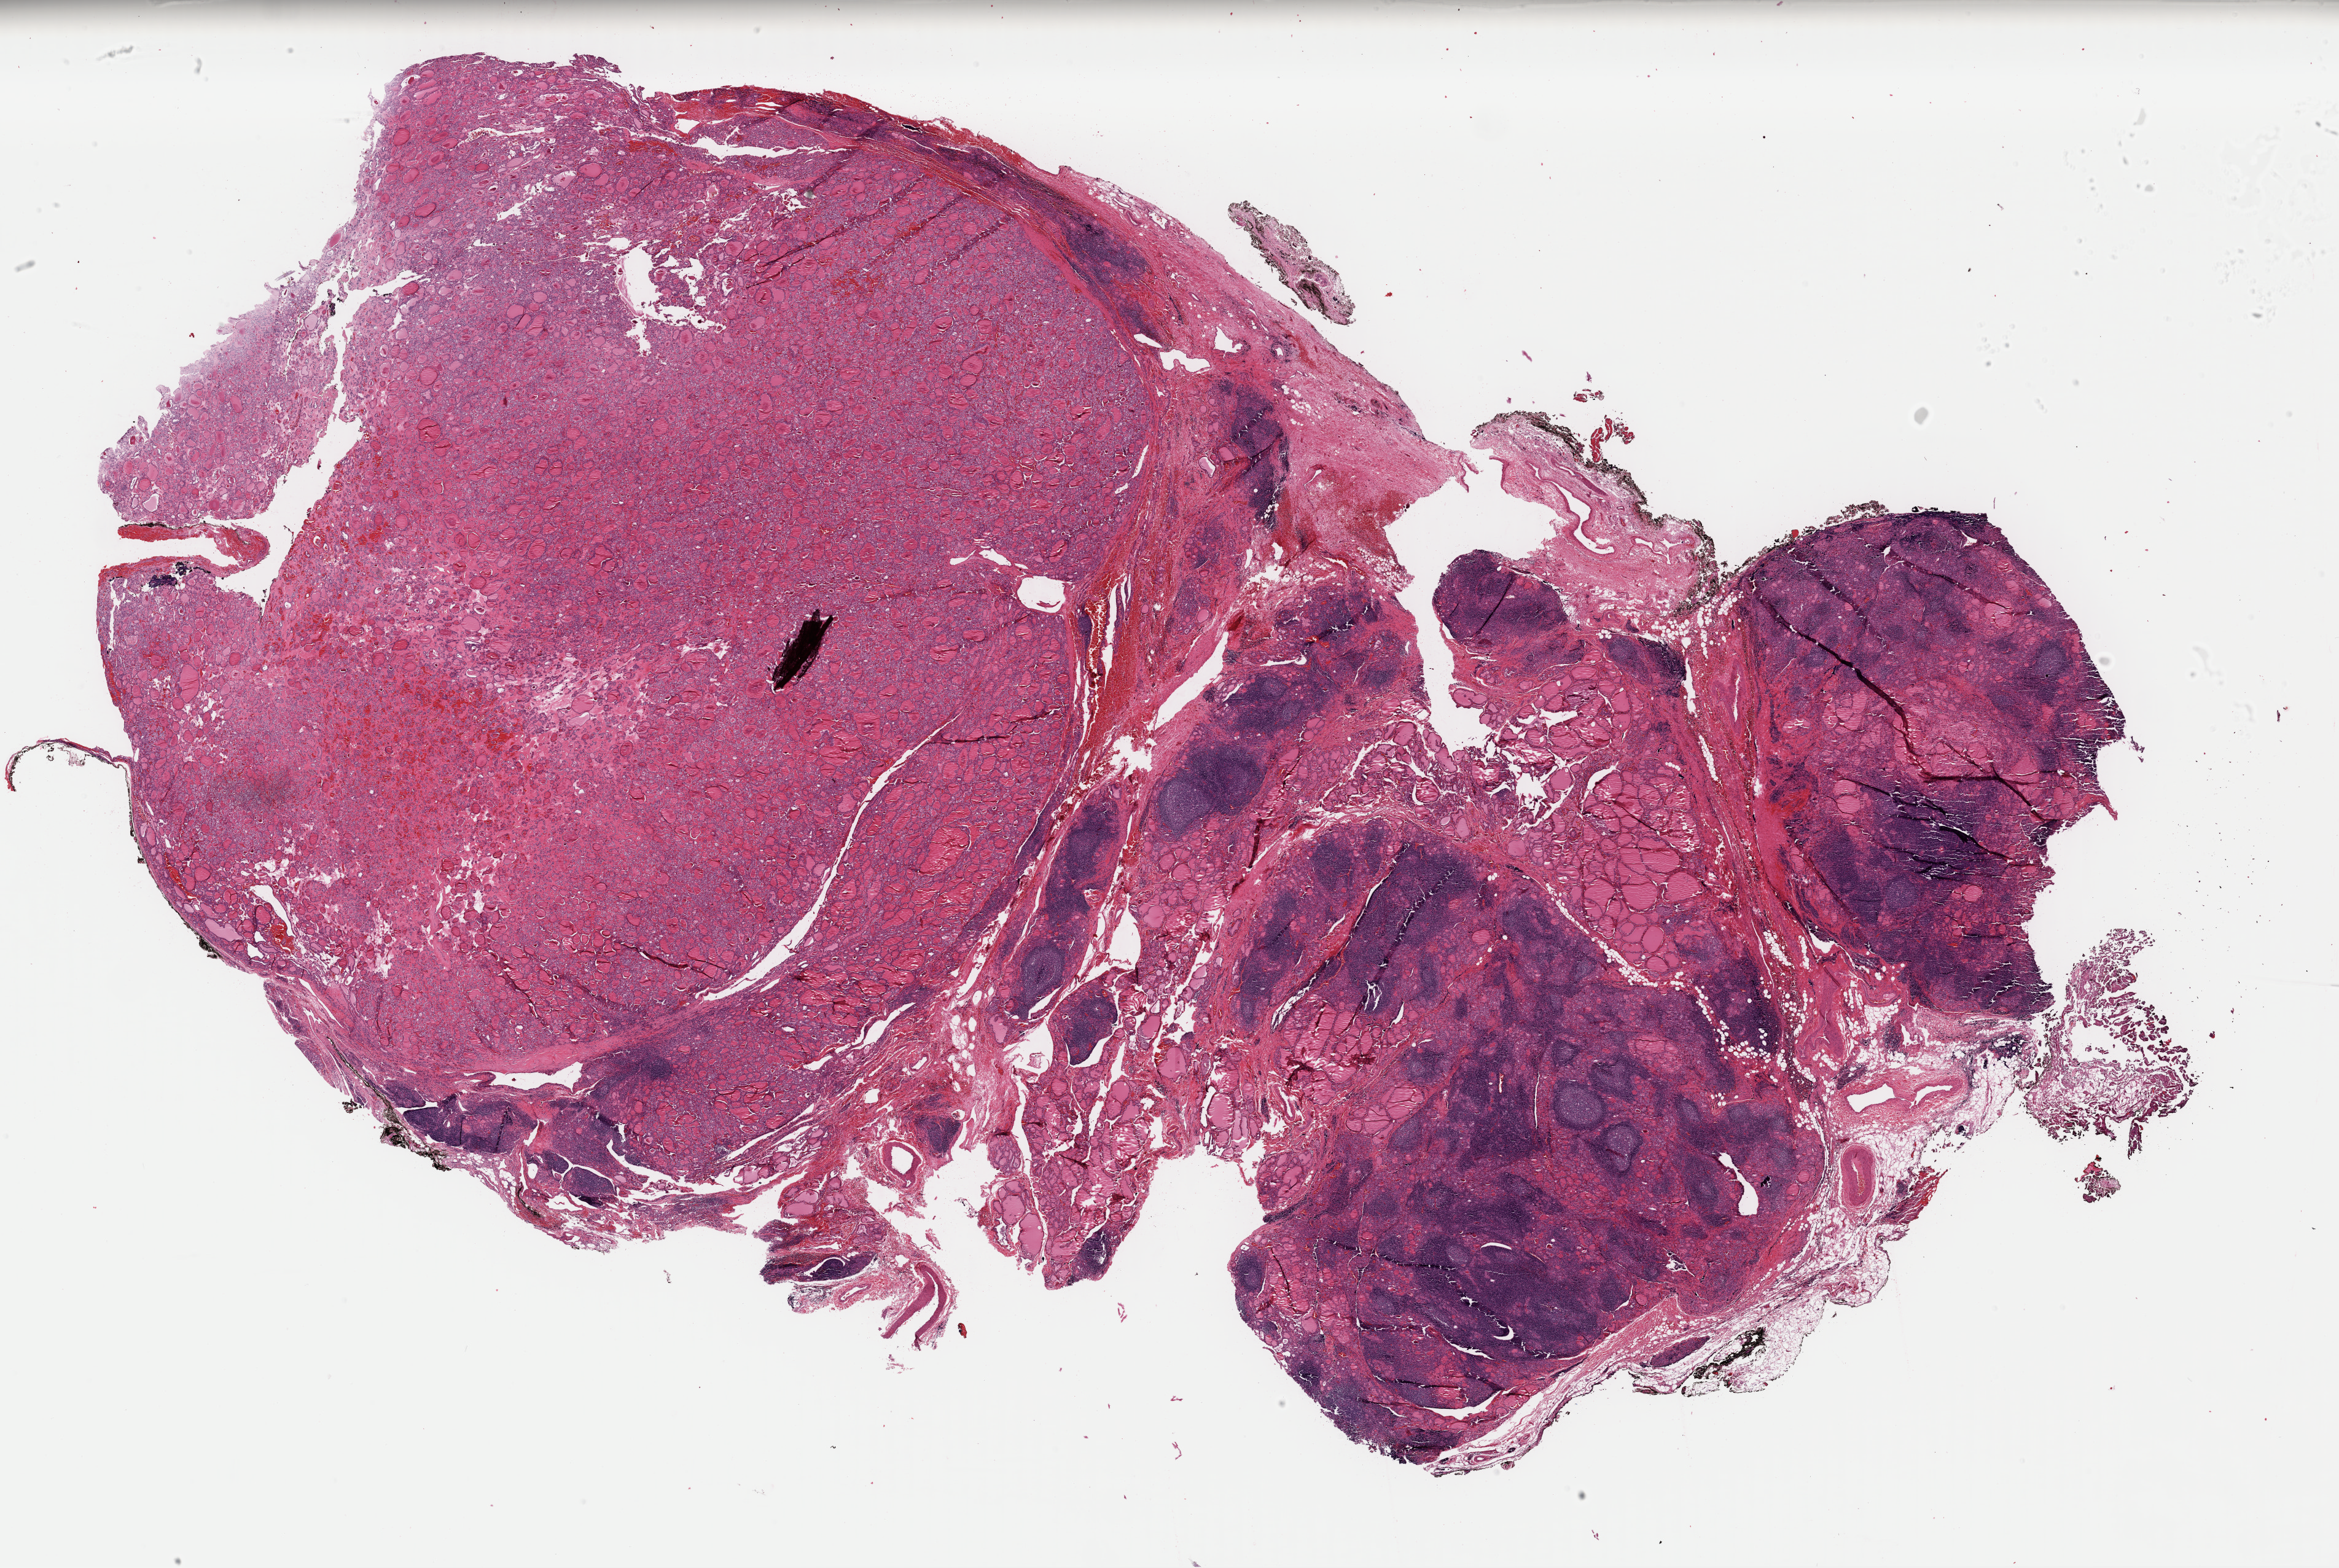
Whole-slide histology image, H&E, whole scanned area (about 30.1 x 20.2 mm, from a 40x scan) shown as a low-resolution overview; FFPE section; thyroid, primary tumour sample. Male, age 33 years at initial diagnosis.
* AJCC pathologic stage: I (7th edition)
* lymph nodes positive (case pathology): 0 of 8 examined
* TNM: T2 N0 M0
* laterality: left
* histologic diagnosis: Papillary carcinoma, follicular variant (thyroid gland)